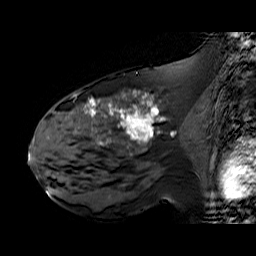
Breast MRI (dynamic contrast-enhanced), one sagittal slice; position 32 of 60 along the scan axis; dynamic contrast-enhanced series, time point 2 of 6 at this slice position (early post-contrast); 1.5 T; TE 6.3 ms, TR 32.9 ms; 4 mm slice thickness; 256 × 256 image matrix. Female patient. From the clinical record (not read from this slice): setting: breast cancer imaged before/during neoadjuvant chemotherapy; receptor status: HER2-positive.
Structures marked on this image (semi-automatically segmented with operator editing):
- analysis volume of interest (the breast-tissue region the enhancement analysis was run in; not a lesion): bounding box <48,92,195,174> (left, top, right, bottom; pixels)
- tumour enhancement mask (voxels above the 100 % enhancement threshold inside the analysis volume of interest): <85,92,154,143>